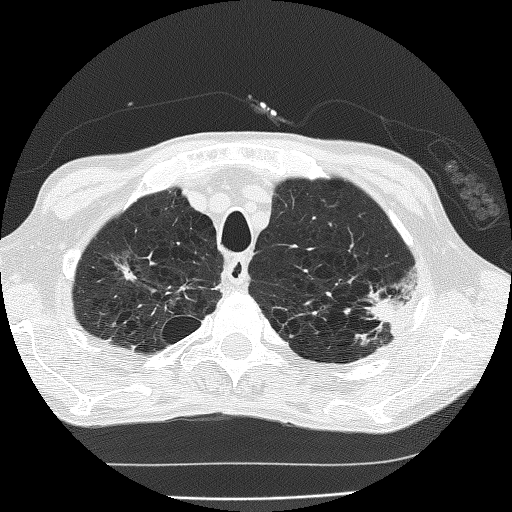
Low-dose screening chest CT, axial slice, second annual screen, lung window (W 1500 / L -600 HU), 512 × 512 image matrix. Male, age 60 years at enrolment.
• Lesion marked by an expert reader, bounding box <346,276,418,342> (left, top, right, bottom; pixels).
• The screening reader recorded 2 non-calcified nodules or masses ≥4 mm on this exam (left upper lobe, left upper lobe); which of them this box marks is not recorded.
• Official screen result: positive, other.
• Participant outcome: lung cancer diagnosed 178 days after this screen — bronchiolo-alveolar carcinoma, mucinous, left upper lobe, stage IV (AJCC 6th edition).